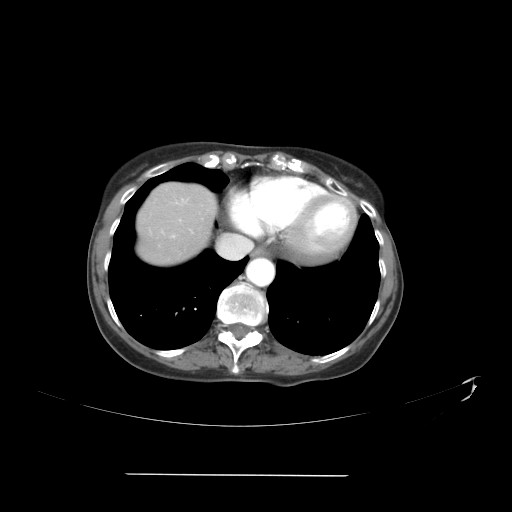
Contrast-enhanced abdominal CT, one axial slice; slice 36 of 41 in the series (ordered by position); reconstruction kernel STANDARD; 120 kVp; intravenous contrast given; soft-tissue window (W 400 / L 40 HU); 5 mm slice thickness; 512 × 512 image matrix. Female patient, age 74 years. Case-level facts recorded for this patient, not image findings: diagnosis: colorectal cancer liver metastases, imaged before liver resection; multiple liver metastases: yes; largest metastasis: 3.3 cm; disease in both lobes: yes.
Structures marked on this image (outlined manually by an expert reader):
- liver: bounding box (x1, y1, x2, y2) in pixels: (138, 185, 215, 261)
- planned liver remnant (the part of the liver to remain after resection): (139, 185, 215, 250)